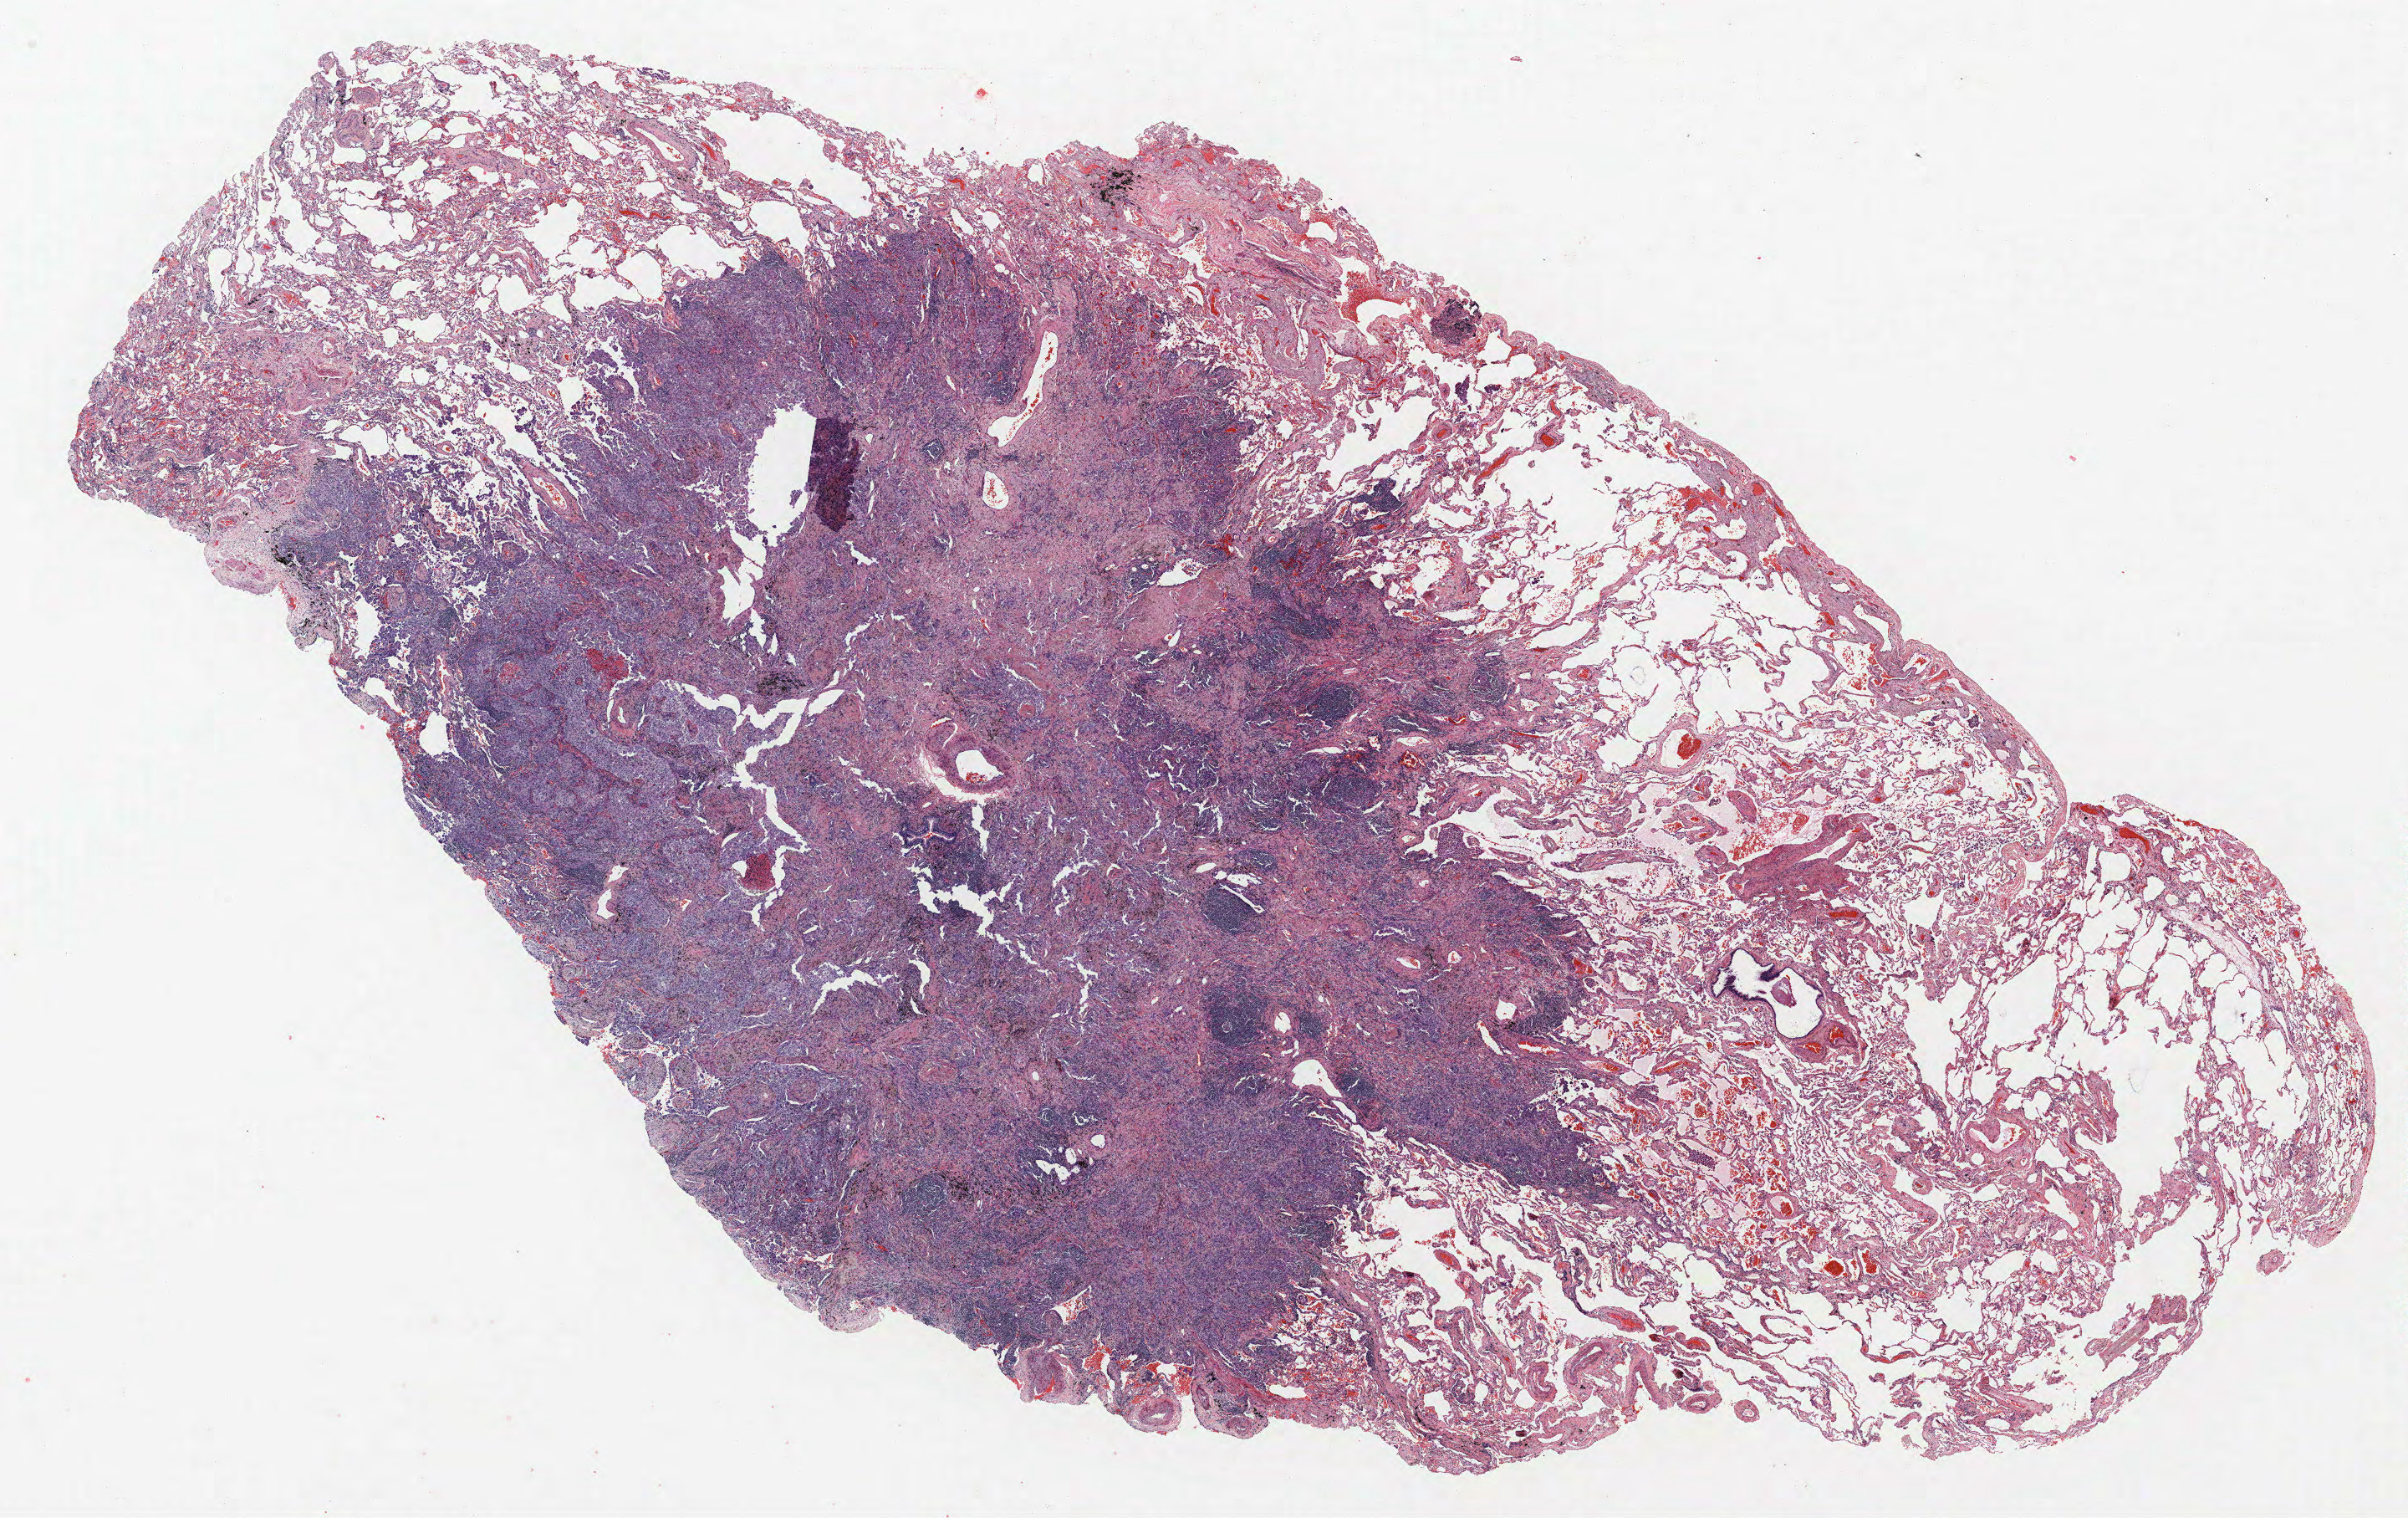
Whole-slide histology image, H&E-stained, low-resolution overview of the scanned area, about 23.0 x 14.5 mm. FFPE section. Lung tissue. Male, age 72 at enrolment. Grade: moderately differentiated (G2).
• stage (AJCC 6th edition): IIA
• tumour size (pathology): 12 mm
• participant's lung-cancer diagnosis: Adenocarcinoma, NOS (ICD-O-3 8140/3)
• primary tumour location (clinical record): right upper lobe